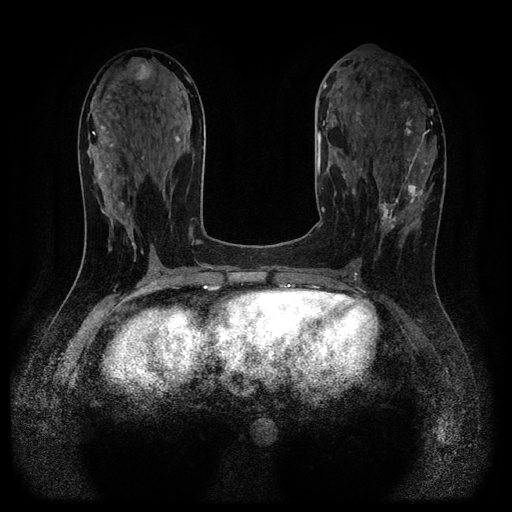
Breast MRI (dynamic contrast-enhanced, multi-phase), one axial slice; slice 49 of 116 in the series (ordered by position); dynamic contrast-enhanced series, time point 2 of 5 at this slice position (early post-contrast); 1.5 T; TE 2.7 ms, TR 5.4 ms; 2.2 mm slice thickness; 512 × 512 image matrix, field of view 330 × 330 mm. Patient: female, 43 years.
Outlined on this slice (semi-automatic segmentation, software-assisted and operator-edited):
- breast lesion (labelled 'tumour' in the annotation; benign lesions carry a separate 'benign' label): bounding box (x1, y1, x2, y2) in pixels: (375, 176, 427, 235)
- breast lesion (labelled benign in the annotation): (121, 57, 153, 81)